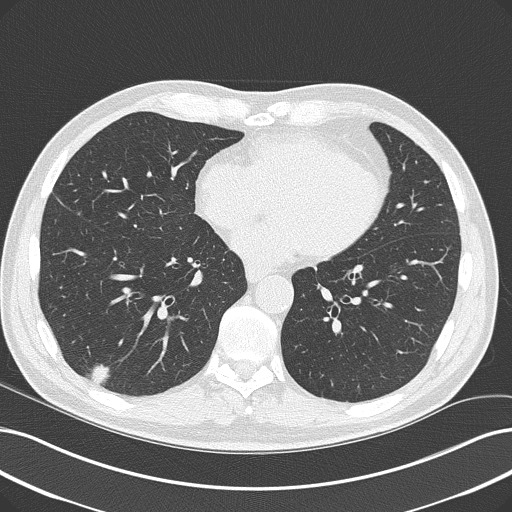
Low-dose screening chest CT, one axial slice. Position 91 of 228 along the scan axis. Lung window (W 1500 / L -600 HU). 2 mm slice thickness. 512 × 512 image matrix, field of view 366 × 366 mm.
Outlined on this slice (expert manual segmentation):
- lesion 1 (tumor, lower lobe of right lung): box from (x=89, y=364) to (x=110, y=384) px